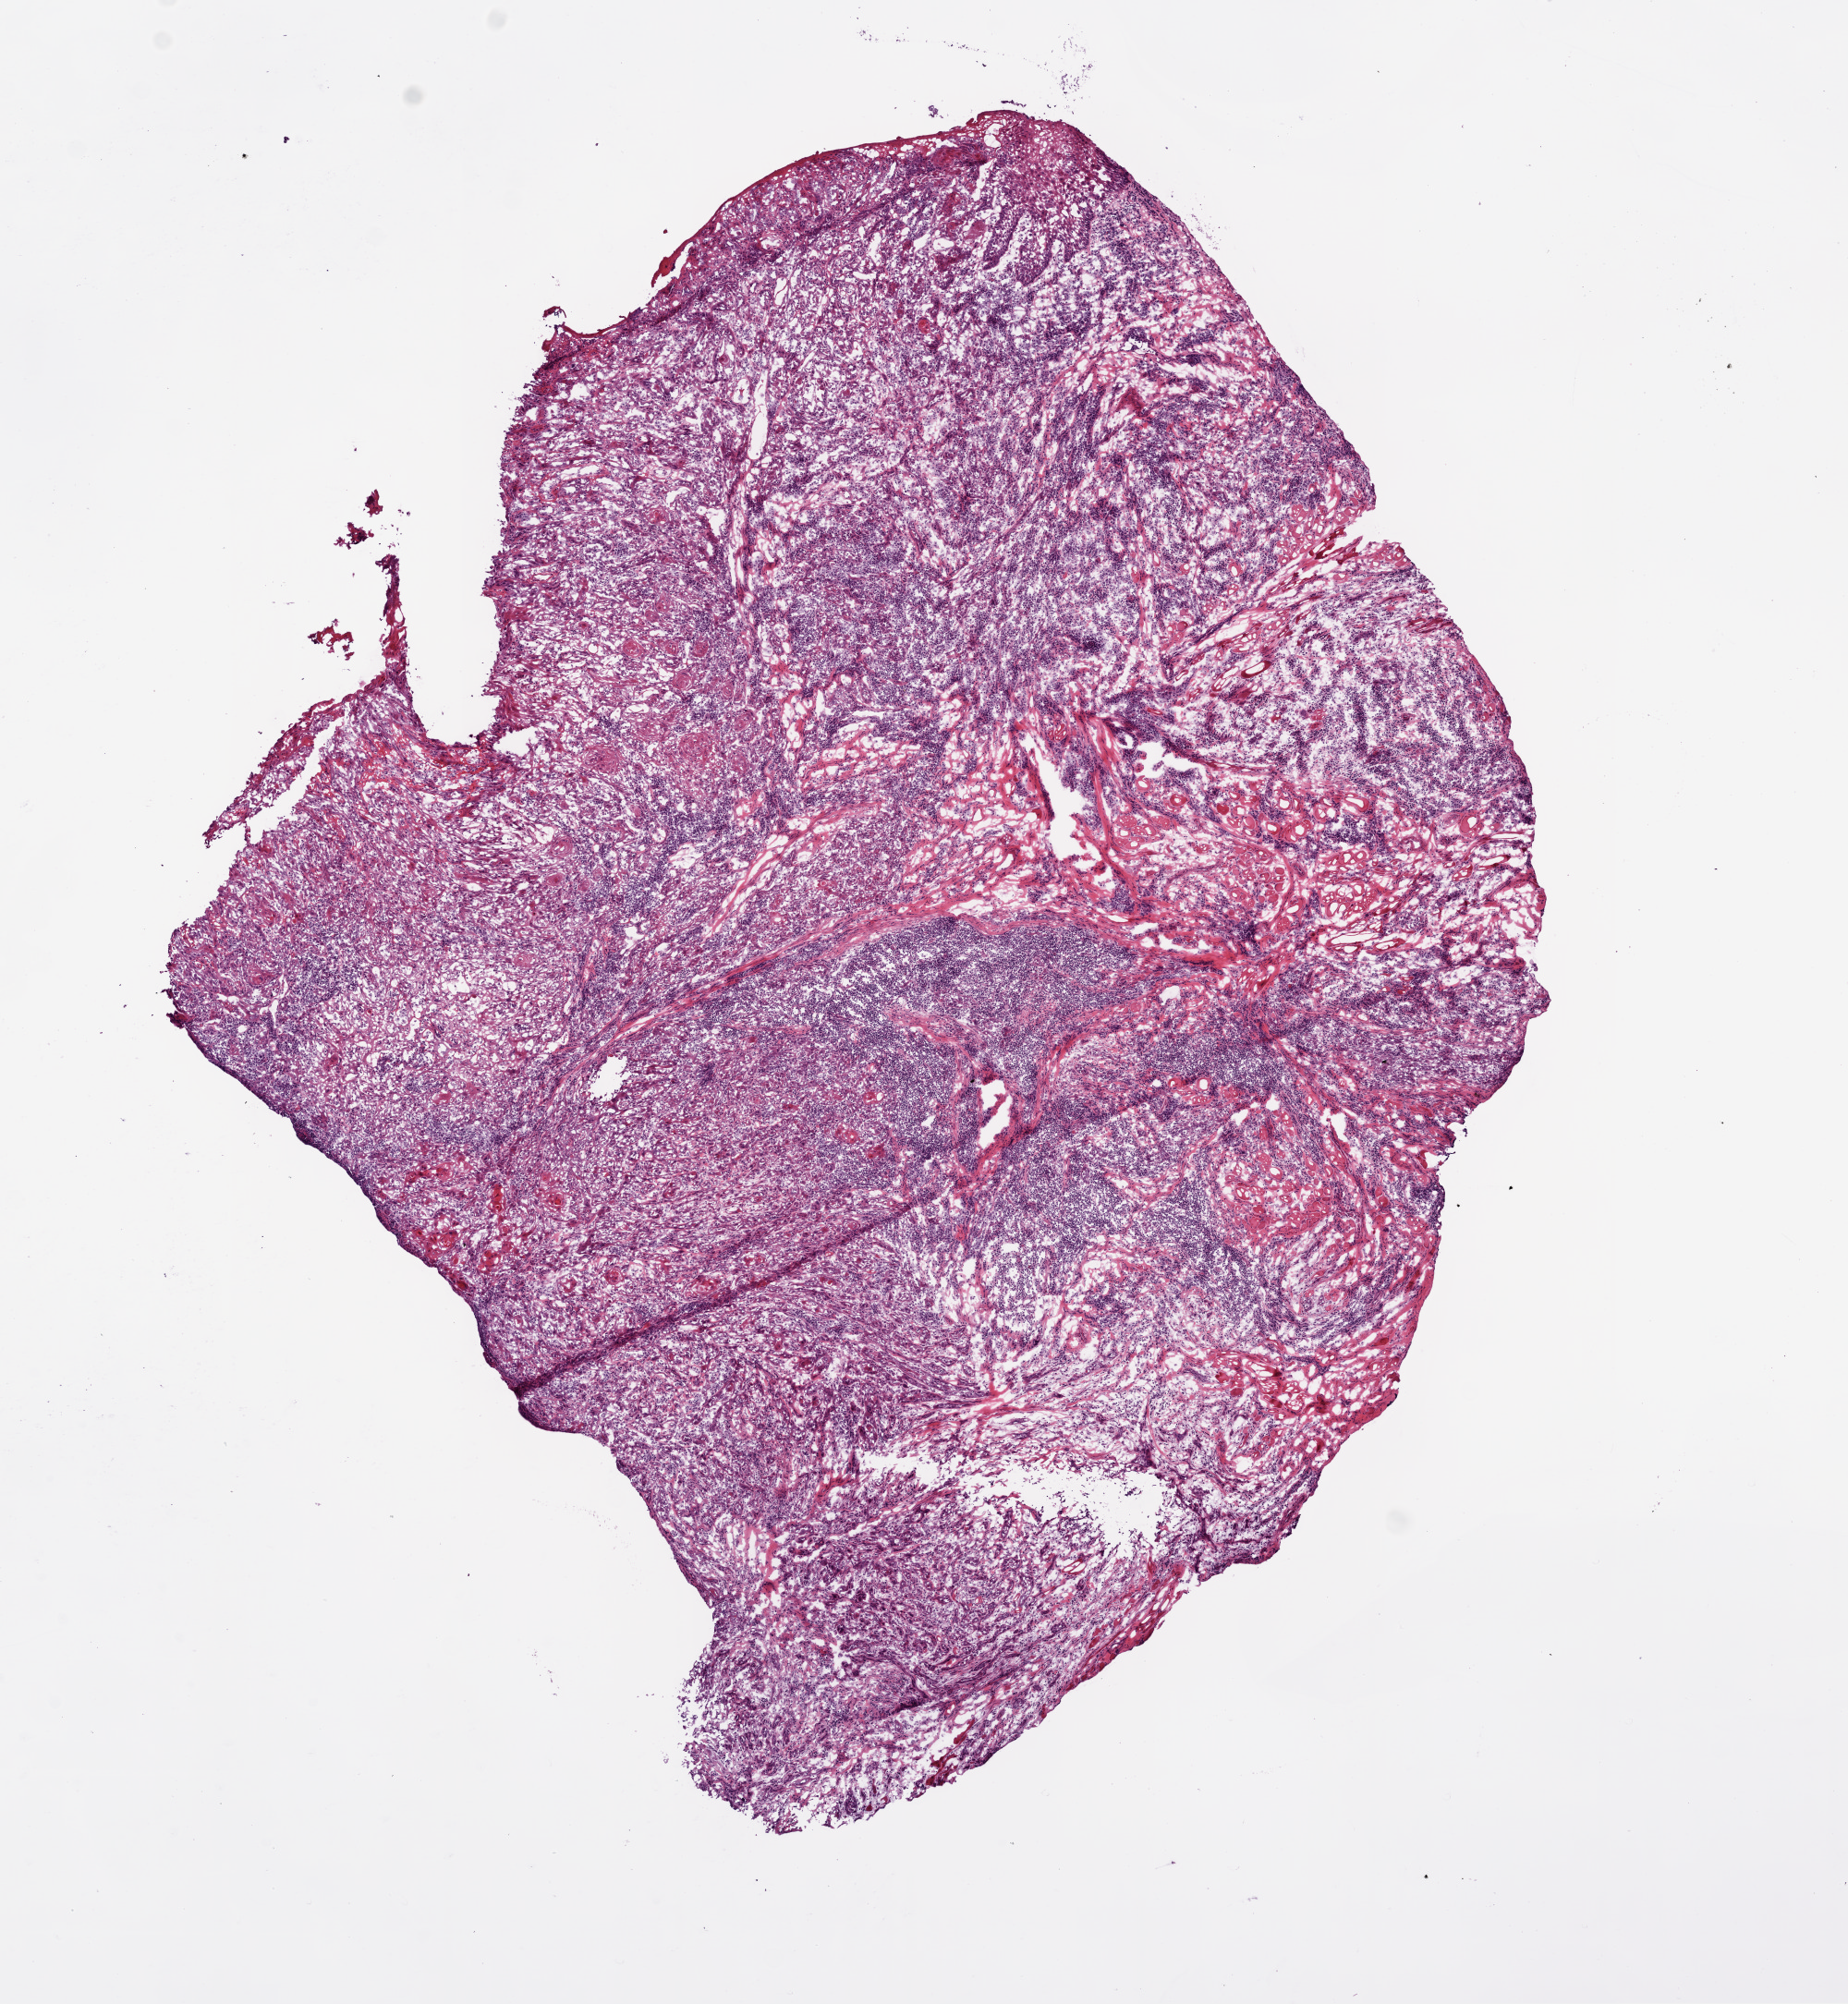
Digitized H&E tissue section (whole slide) — shown as a low-resolution overview of the whole scanned area (about 8.0 x 8.7 mm), frozen section from the bottom of the tissue portion, head and neck, primary tumour sample. Male patient; age at initial diagnosis 61 years. Histologic grade: G3 (poorly differentiated). Composition of this section per pathologist review: tumour cells 90%, tumour nuclei 40%, normal cells 0%, stromal cells 10%, necrosis 0%. Infiltration values recorded for this section: lymphocyte infiltration 50%, monocyte infiltration 0%, neutrophil infiltration 5%.
Diagnosis: Squamous cell carcinoma, NOS (tongue, NOS). TNM: T1 N1. AJCC pathologic stage: III.